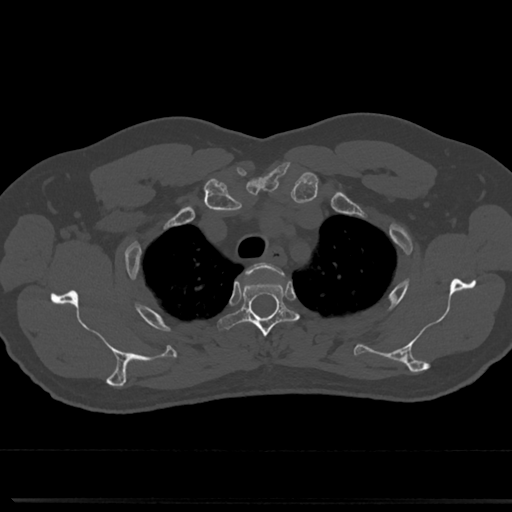
CT including the spine, one axial slice; position 598 of 817 along the scan axis; bone window (W 1800 / L 400 HU); 0.5 mm slice thickness; 512 × 512 image matrix, field of view 355 × 355 mm. Patient: male, 61 years. Case-level facts recorded for this patient, not image findings: primary cancer: prostate.
Annotated regions visible in this slice (semi-automatically segmented with operator editing):
- T2 vertebra: bounding box (x1, y1, x2, y2) in pixels: (272, 266, 276, 269)
- T3 vertebra: (225, 267, 295, 344)